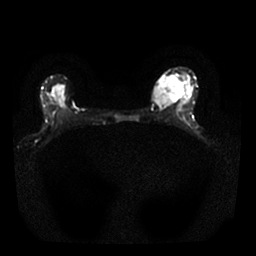
Breast MRI, one axial slice. Slice 14 of 25 in the series (ordered by position). Diffusion-weighted series; image 2 of 4 stored at this slice position (different b-values; order by instance number). 1.5 T. 256 × 256 image matrix. Female patient.
Annotated regions visible in this slice (expert manual segmentation):
- tumour on diffusion-weighted imaging: box from (x=155, y=77) to (x=182, y=105) px